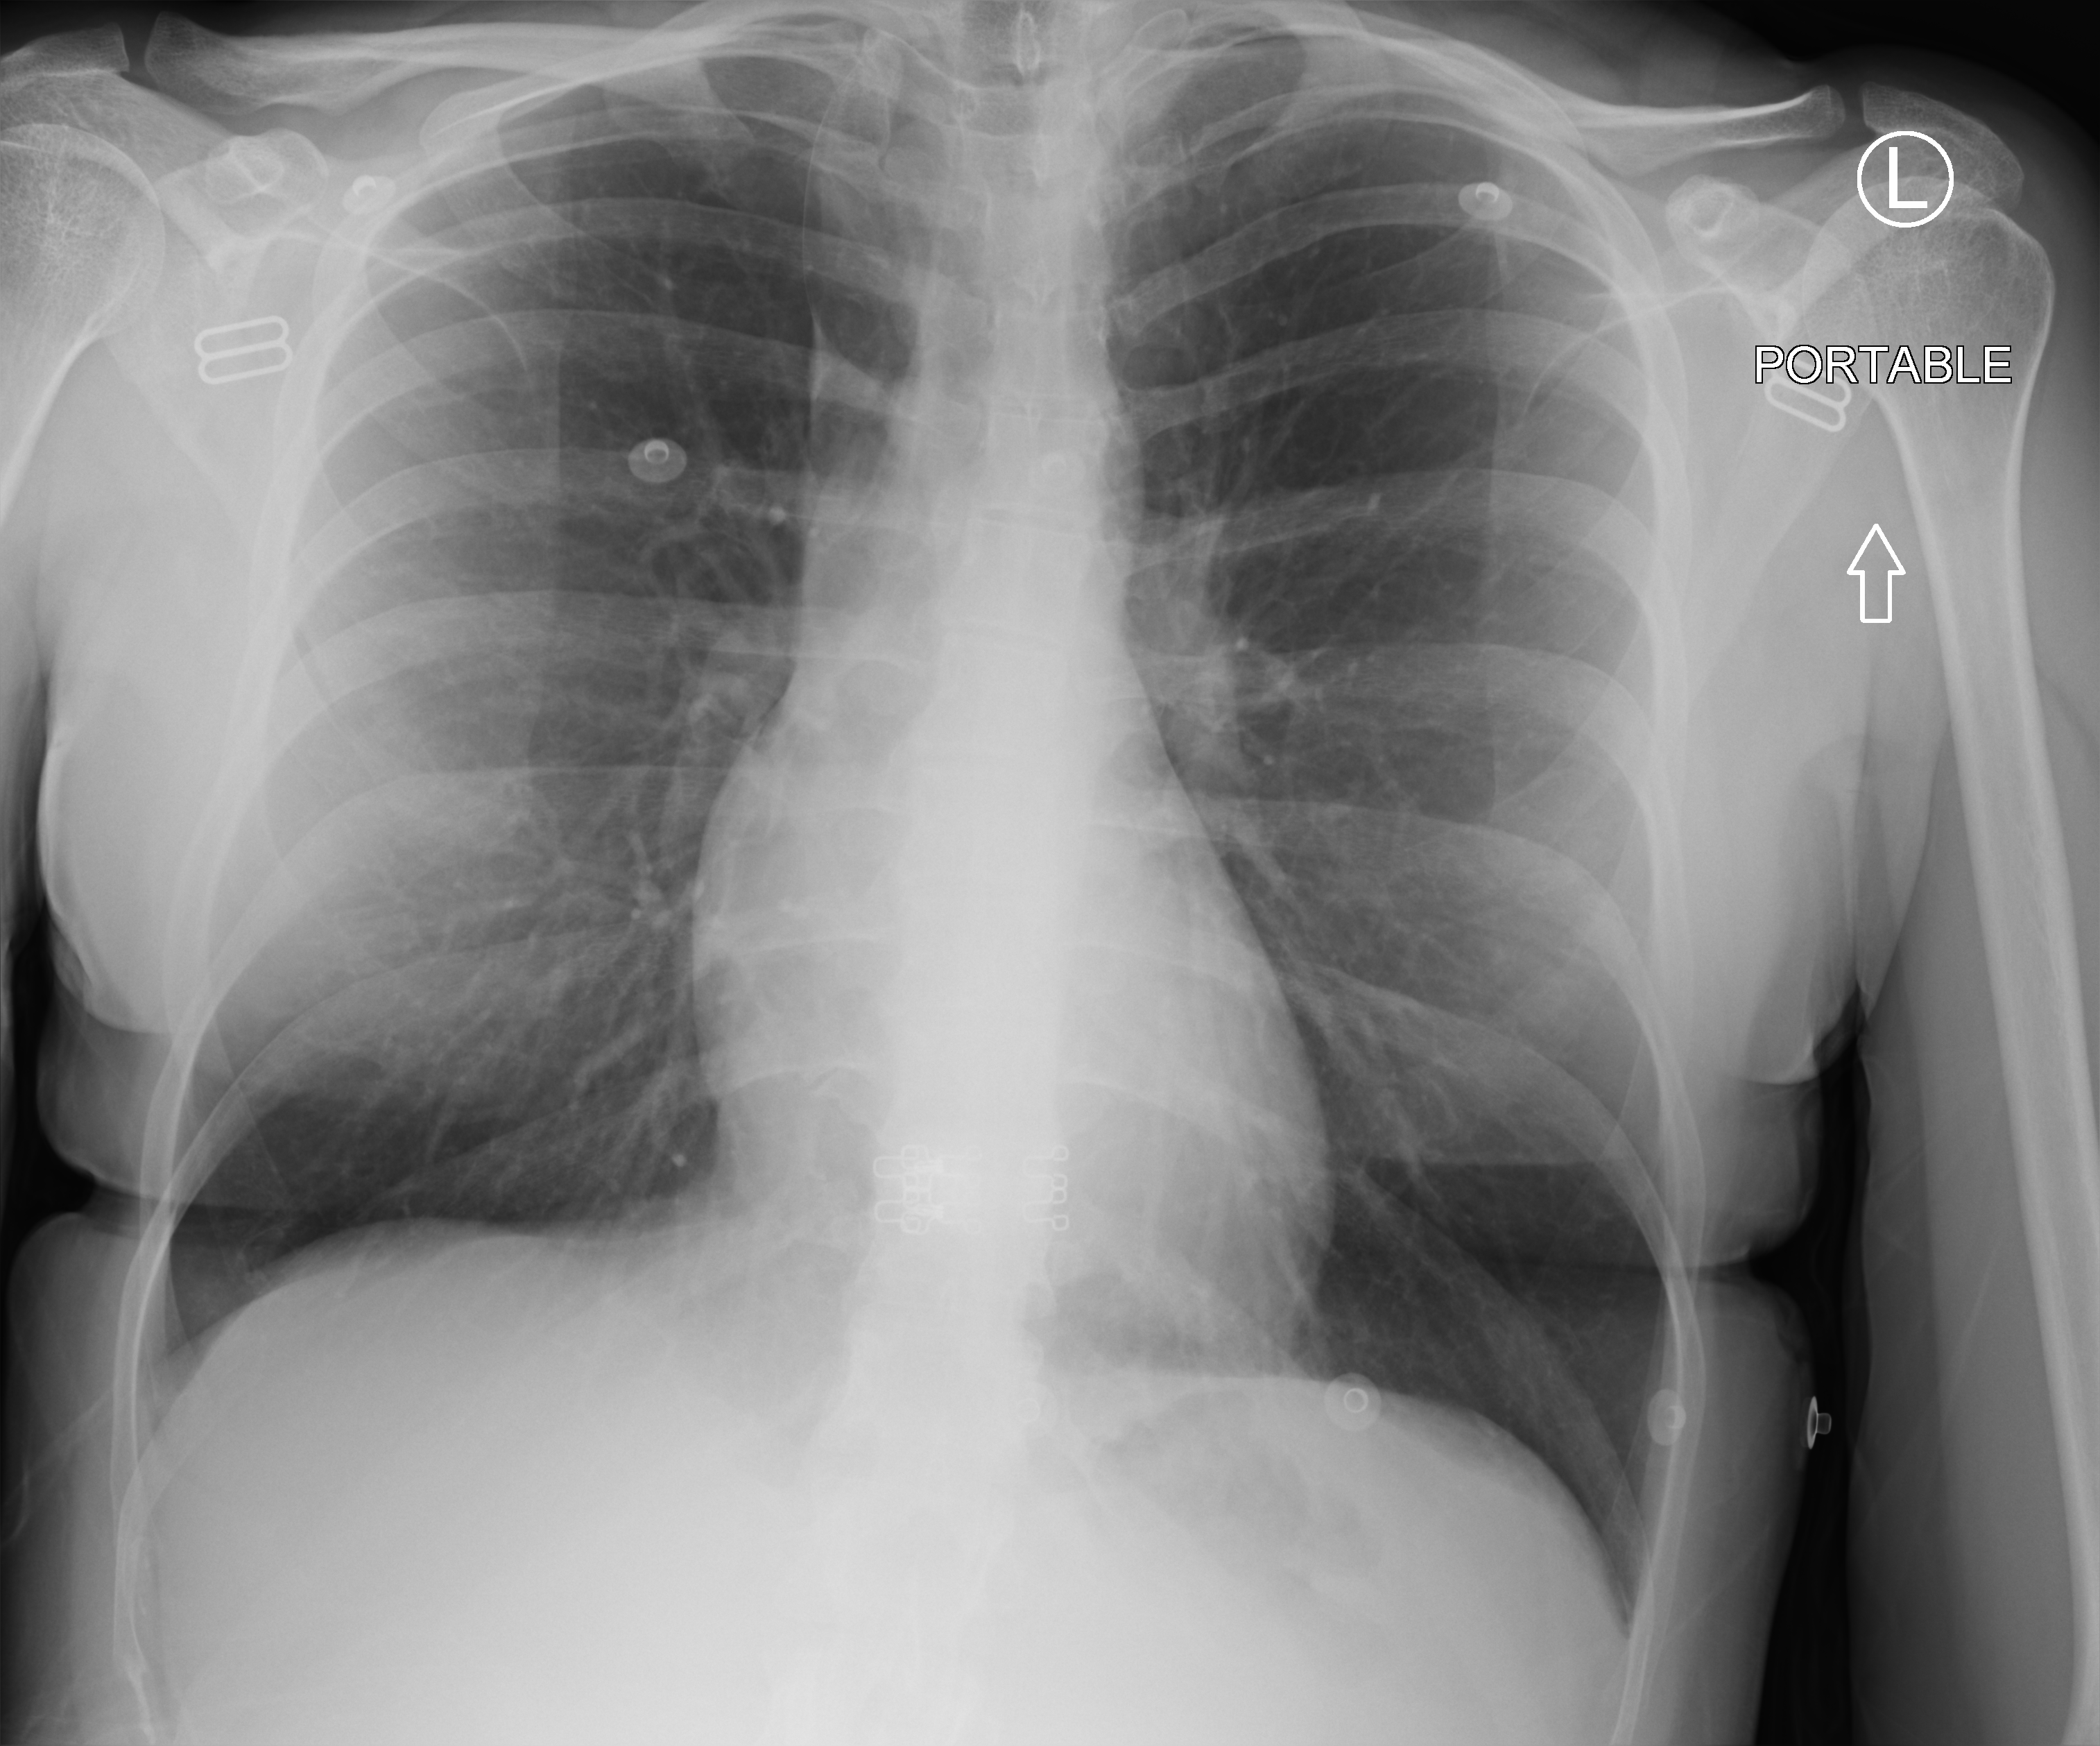
Portable chest radiograph, anteroposterior (AP) projection. Patient hospitalised with COVID-19; female, aged 18–59 years.
Admission-level facts for this patient (not findings on this image; timing relative to this image not recorded):
- length of hospital stay: 1 day
- admitted to intensive care during this hospital stay: no